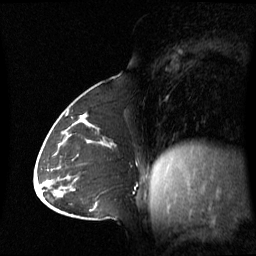
Breast MRI (dynamic contrast-enhanced), one sagittal slice. Position 28 of 60 along the scan axis. Dynamic contrast-enhanced series, image 2 of 3 at this slice position (ordered by acquisition). 1.5 T. TE 4.2 ms, TR 8.4 ms. 2.8 mm slice thickness. 256 × 256 image matrix. Female patient, age 43 years. Case-level facts recorded for this patient, not image findings: setting: breast cancer imaged before/during neoadjuvant chemotherapy; receptor status: triple-negative.
Outlined on this slice (semi-automatically segmented with operator editing):
- analysis volume of interest (the breast-tissue region the enhancement analysis was run in; not a lesion): bounding box <62,124,114,180> (left, top, right, bottom; pixels)
- tumour enhancement mask (voxels above the 70 % enhancement threshold inside the analysis volume of interest): <86,124,88,142>